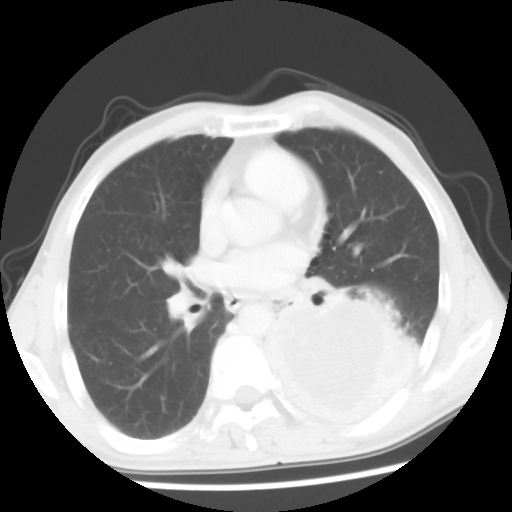
Chest CT, one axial slice. Position 29 of 56 along the scan axis. Lung window (W 1500 / L -600 HU). 5 mm slice thickness. 512 × 512 image matrix. Male patient, age 60 years. Case-level facts recorded for this patient, not image findings: clinical TNM (as recorded): T4 N0 M0.
Outlined on this slice (rectangle marked by the reading radiologist):
- lung tumour (recorded histology: squamous cell carcinoma): bounding box [x1, y1, x2, y2] px = [245, 288, 430, 436]